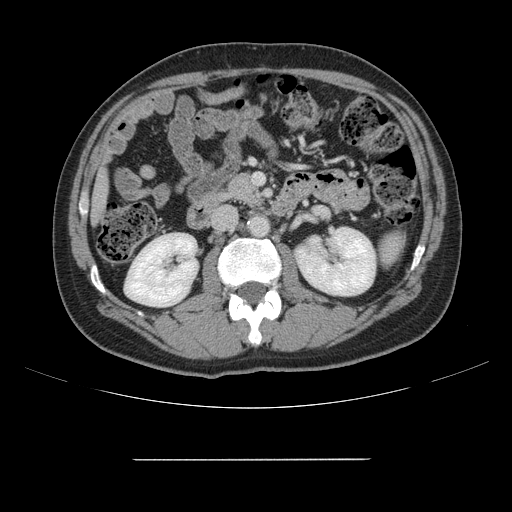
Contrast-enhanced abdominal CT, one axial slice. Slice 54 of 164 in the series (ordered by position). 120 kVp. Intravenous contrast given. Soft-tissue window (W 400 / L 40 HU). 2.5 mm slice thickness. 512 × 512 image matrix, field of view 404 × 404 mm. Male patient, age 54 years. Case-level facts recorded for this patient, not image findings: diagnosis: colorectal cancer liver metastases, imaged before liver resection; multiple liver metastases: yes; largest metastasis: 1 cm; disease in both lobes: no.
Structures marked on this image (expert manual segmentation):
- liver: bounding box [x1, y1, x2, y2] px = [93, 175, 106, 217]
- planned liver remnant (the part of the liver to remain after resection): [93, 176, 106, 219]